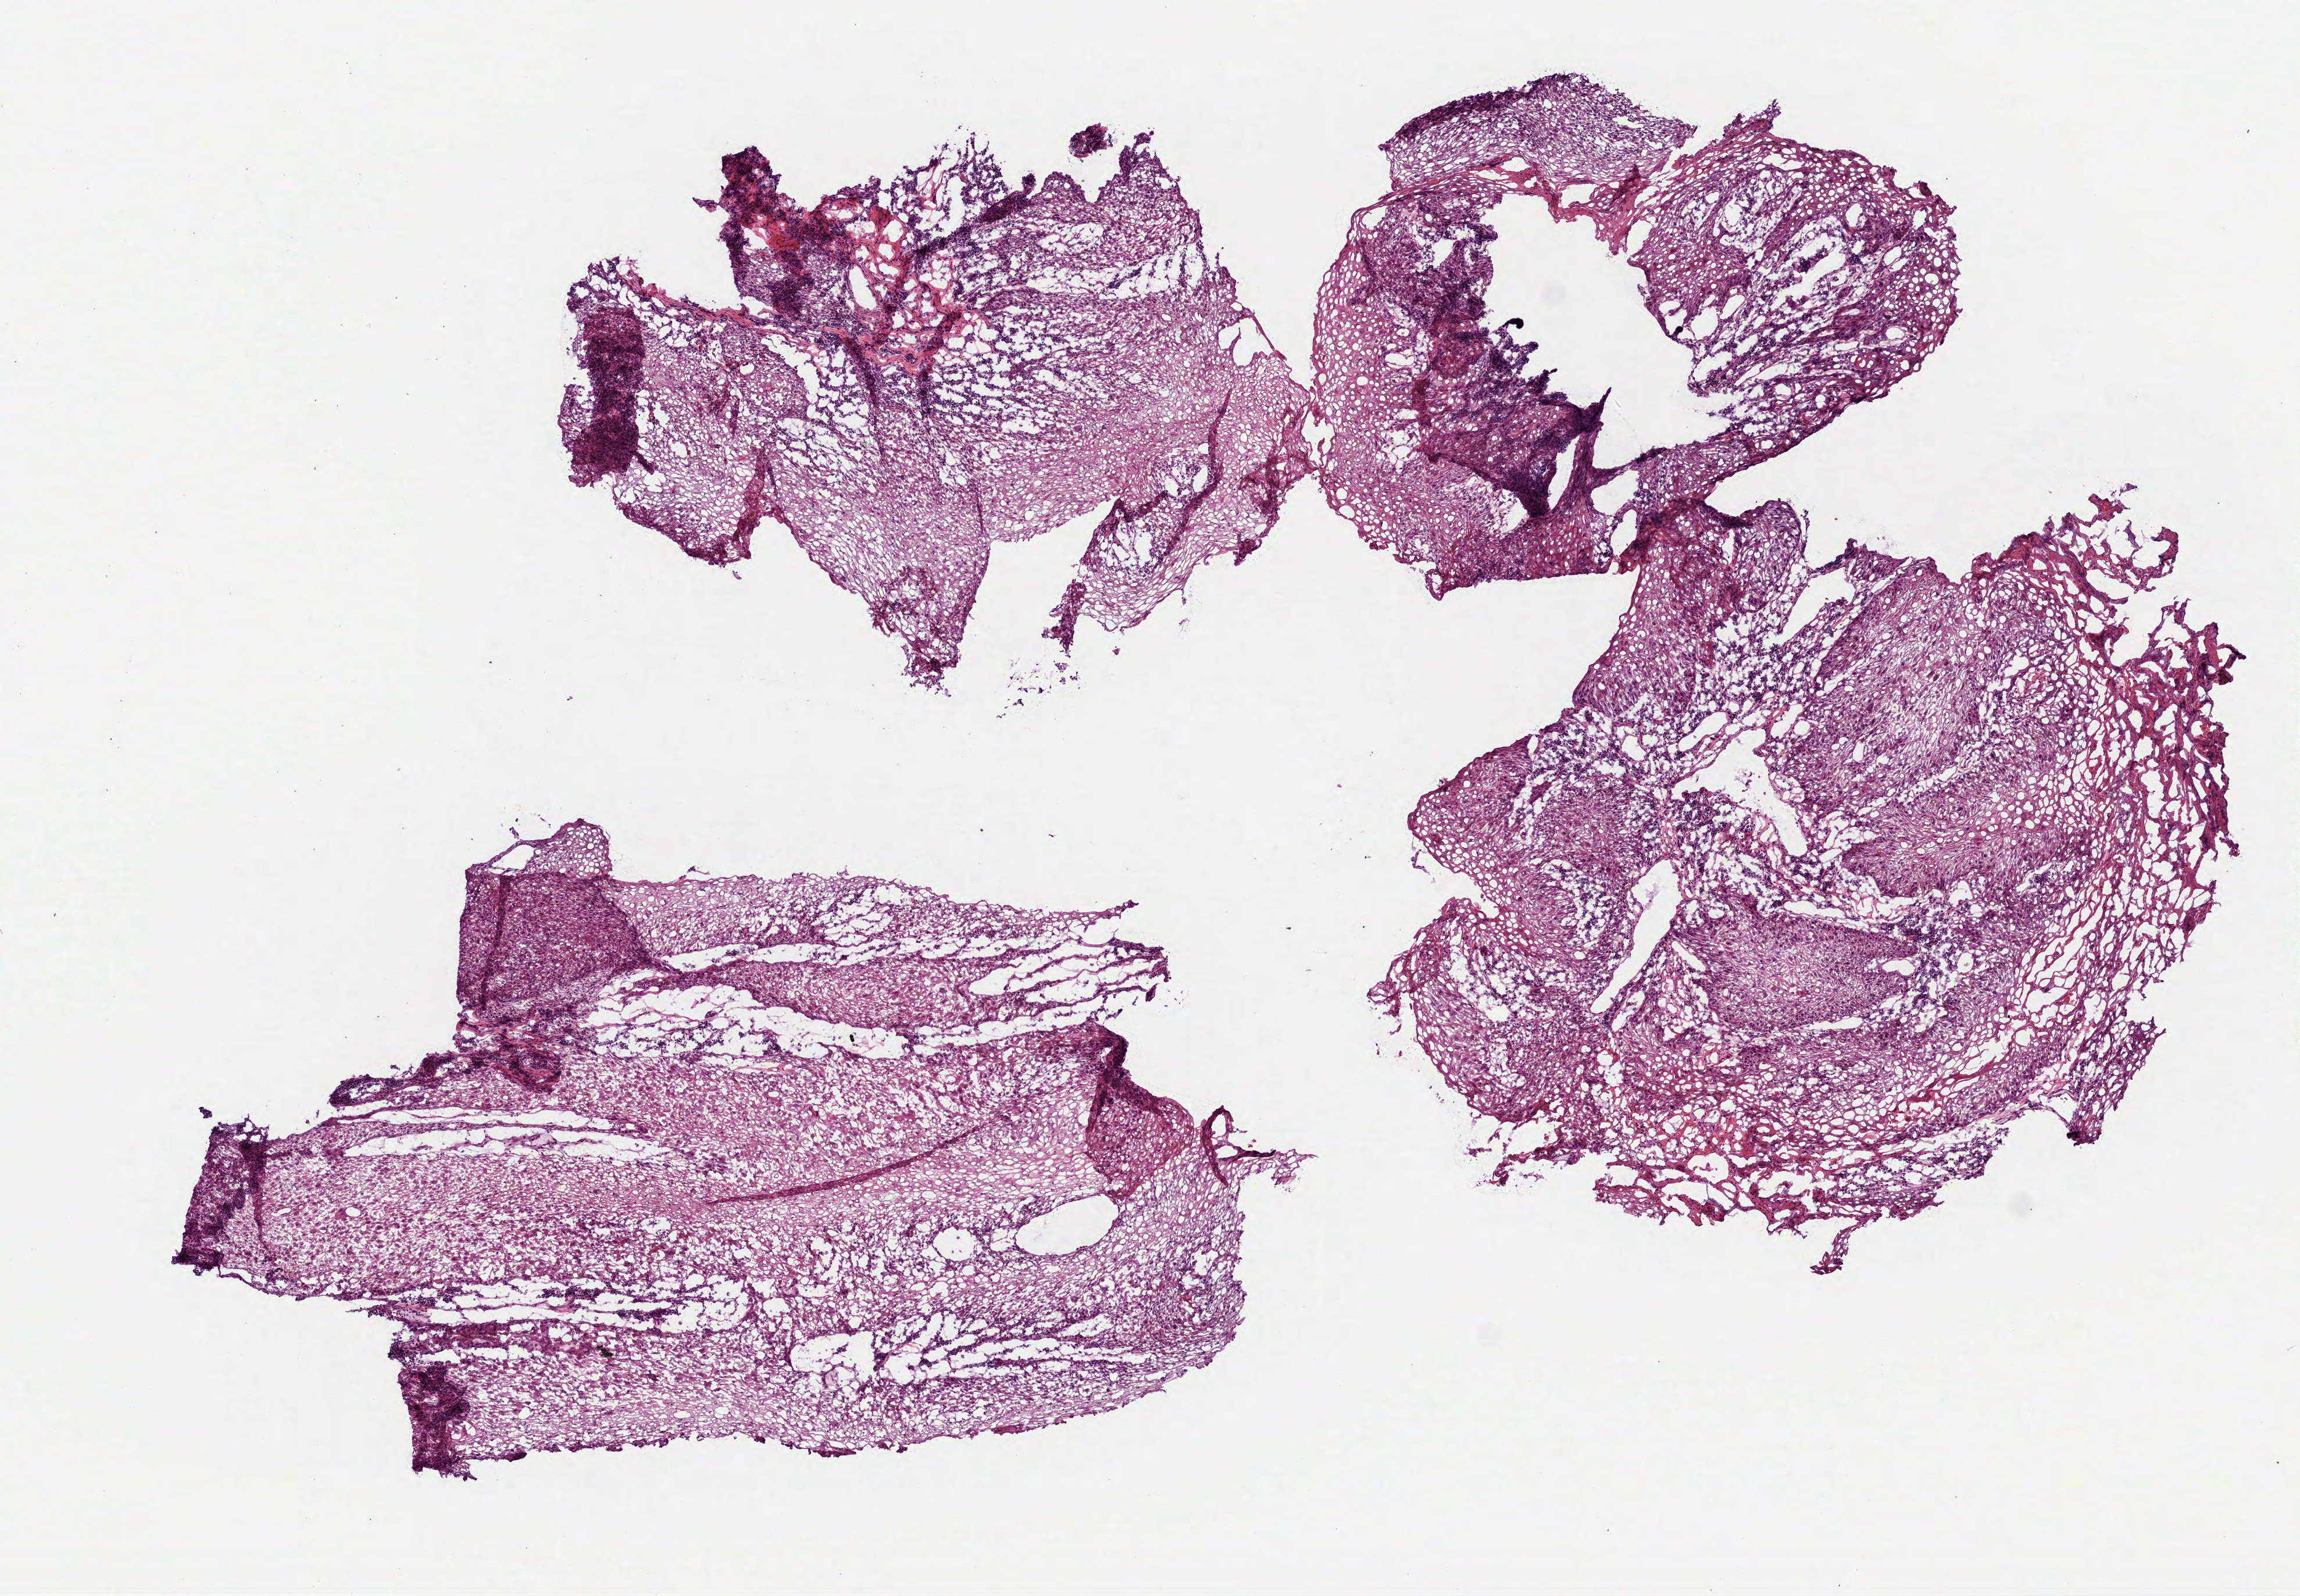
Digitized H&E-stained tissue section (whole slide) — whole scanned area (about 8.0 x 5.5 mm, slide scanned at 40x) shown as a low-resolution overview. Frozen section from the top of the tissue portion. Head and neck, primary tumour sample. Patient: female, age at initial diagnosis 80 years. Histologic grade: G1 (well differentiated). Composition of this section per pathologist review: tumour cells 100%, tumour nuclei 80%, normal cells 0%, stromal cells 0%, necrosis 0%. Inflammatory infiltration, as recorded: lymphocyte infiltration 7%, monocyte infiltration 0%, neutrophil infiltration 4%.
TNM: T3 N0. Diagnosis: Squamous cell carcinoma, NOS (floor of mouth, NOS). AJCC pathologic stage: III (7th edition).